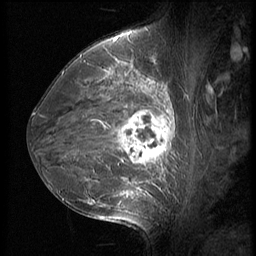
Breast MRI (dynamic contrast-enhanced), one sagittal slice; slice 36 of 56 in the series (ordered by position); 3 images stored at this slice position (order not interpretable as contrast timing); 1.5 T; TE 4.2 ms, TR 9 ms; 2.5 mm slice thickness; 256 × 256 image matrix. Patient: female, 35 years. From the clinical record (not read from this slice): setting: breast cancer imaged before/during neoadjuvant chemotherapy; receptor status: HR-positive, HER2-negative.
Structures marked on this image (semi-automatic segmentation, software-assisted and operator-edited):
- analysis volume of interest (the breast-tissue region the enhancement analysis was run in; not a lesion): box from (x=63, y=60) to (x=190, y=218) px
- tumour enhancement mask (voxels above the 140 % enhancement threshold inside the analysis volume of interest): (x=91, y=65)–(x=174, y=205)